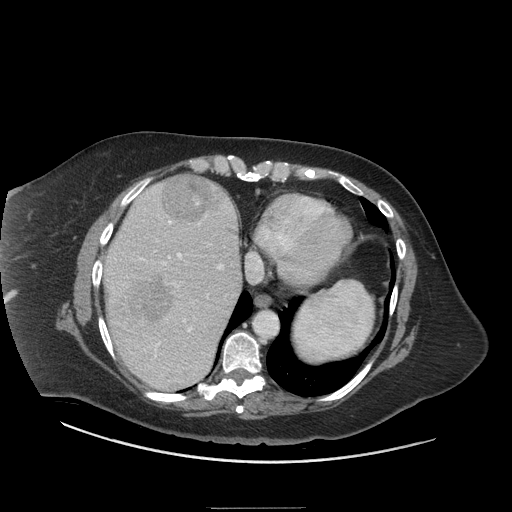
Contrast-enhanced abdominal CT (liver protocol), one axial slice. Slice 57 of 81 in the series (ordered by position). 140 kVp. Soft-tissue window (W 400 / L 40 HU). 512 × 512 image matrix, field of view 440 × 440 mm. Case-level facts recorded for this patient, not image findings: diagnosis: hepatocellular carcinoma (patient treated with transarterial chemoembolisation; whether this scan precedes or follows treatment is not stated here); TNM stage (as recorded): Stage-II; Child-Pugh class: A; tumour differentiation: moderately differentiated; tumour nodularity: multinodular.
Outlined on this slice (semi-automatic segmentation, software-assisted and operator-edited):
- abdominal aorta: bounding box [x1, y1, x2, y2] px = [253, 311, 278, 339]
- liver parenchyma outside the tumour (the mass and vessels are separate outlines, so this box may not span the whole liver): [104, 176, 240, 390]
- mass: [120, 174, 211, 389]
- liver vessels: [114, 215, 224, 368]